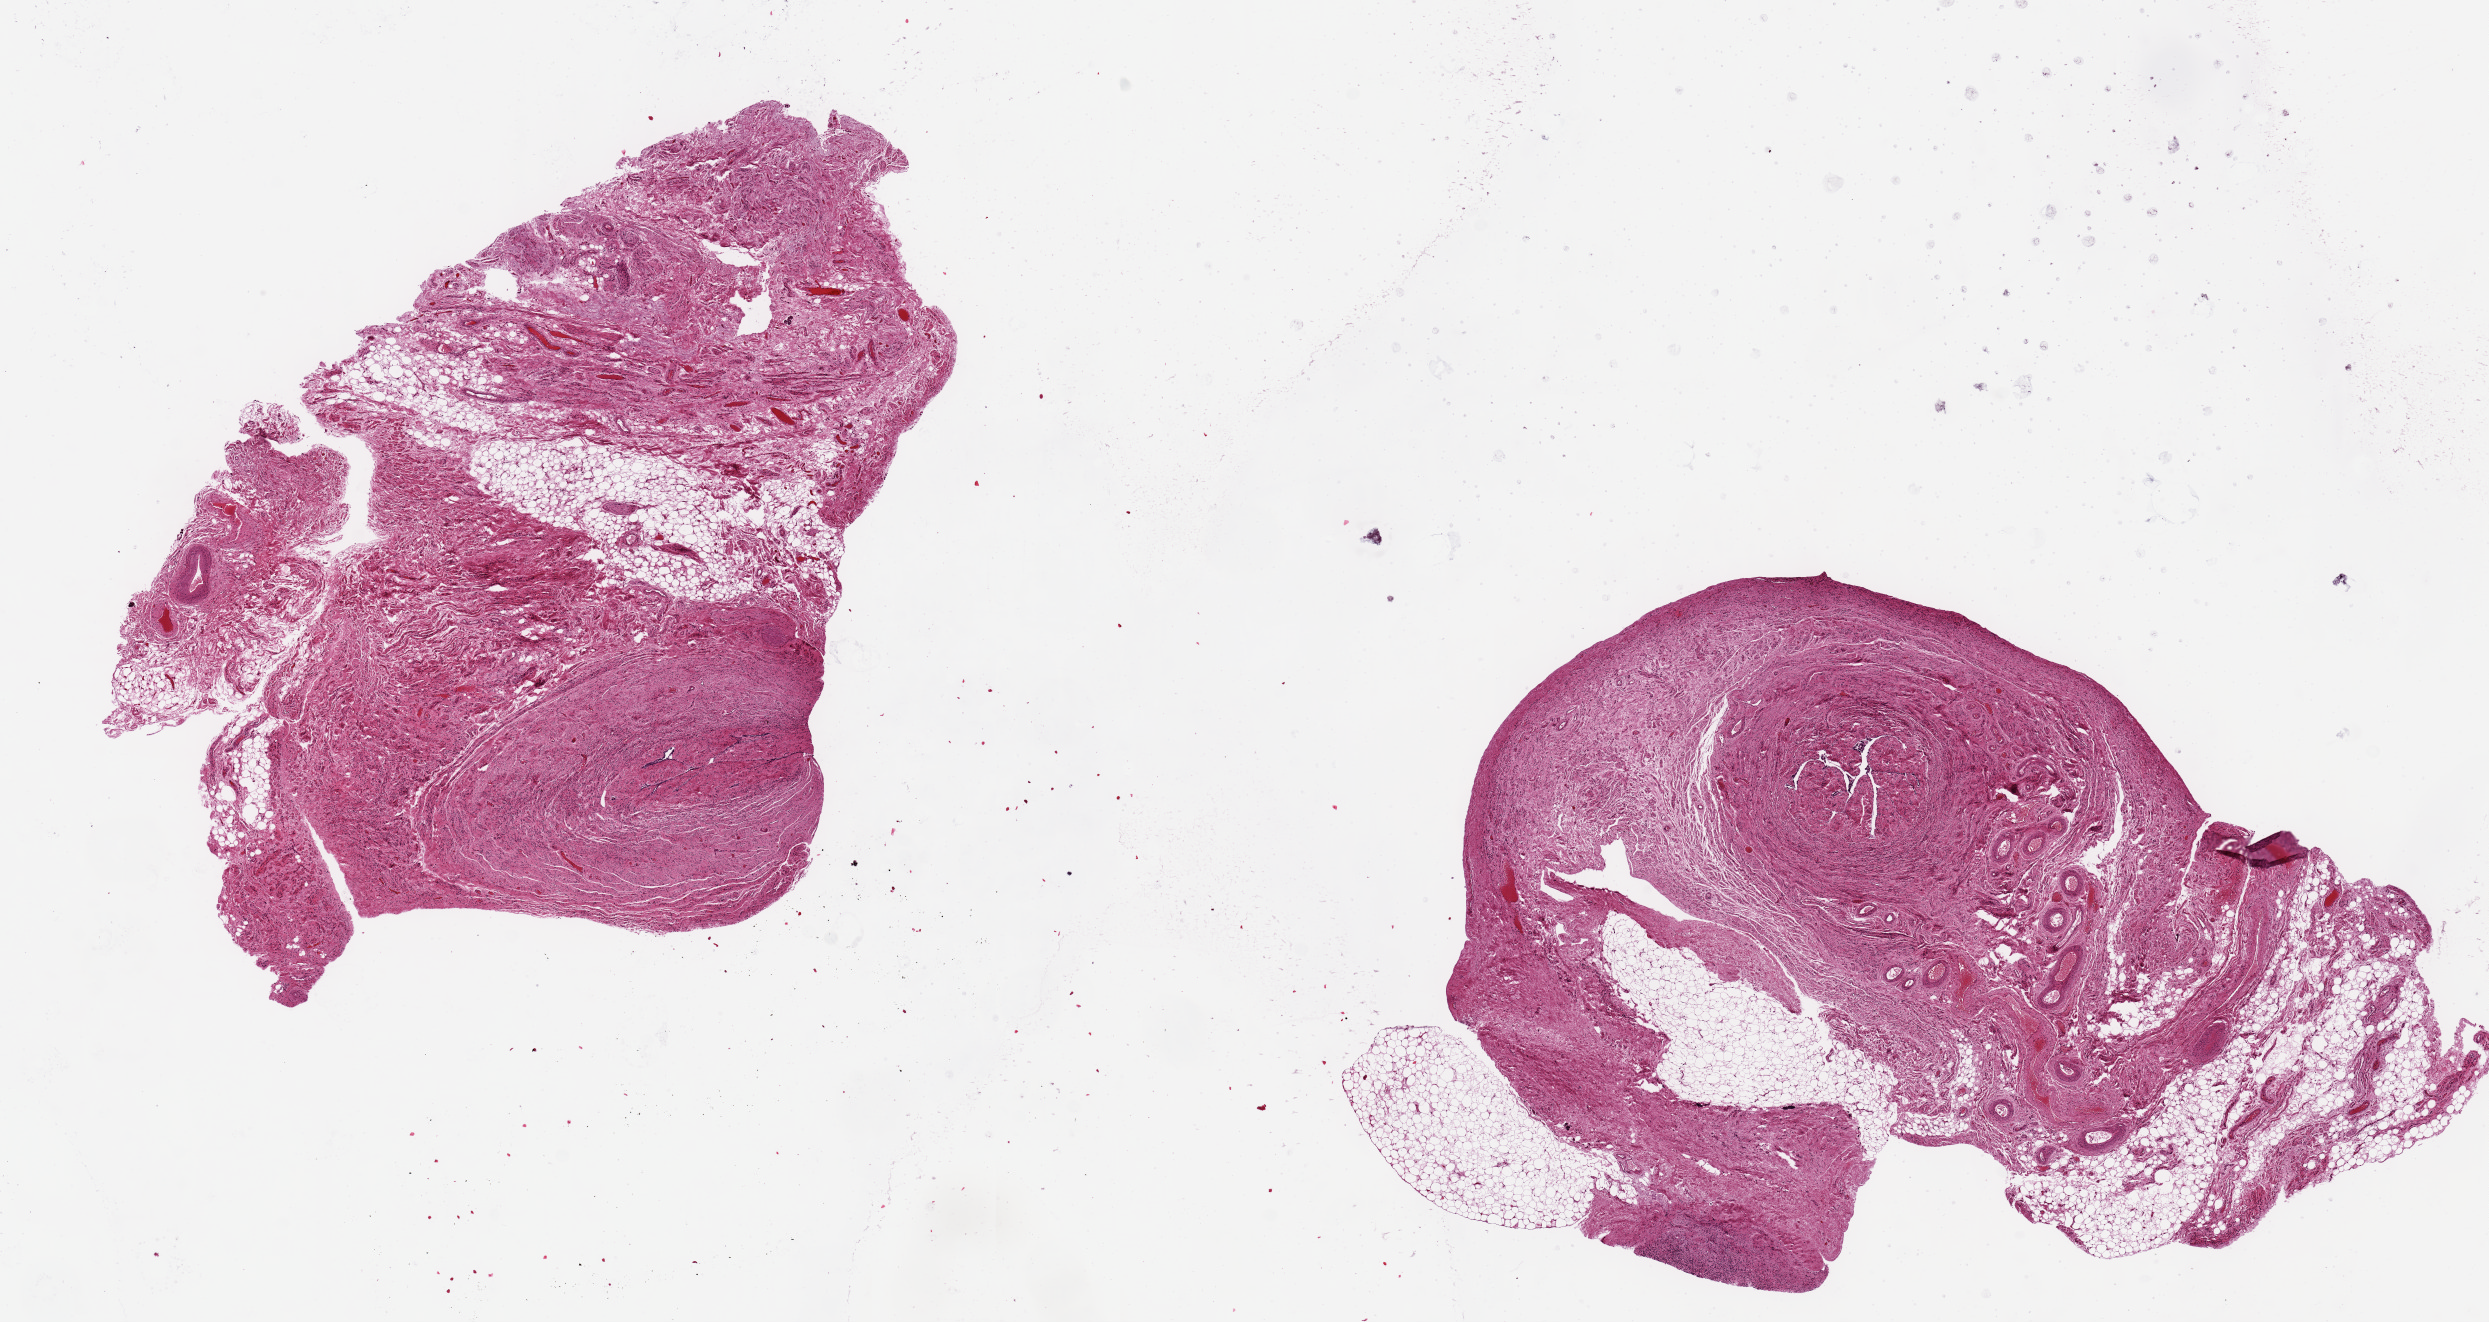
Digitized hematoxylin and eosin (H&E)-stained section — whole scanned area (about 19.7 x 10.5 mm, from a 20x scan) shown as a low-resolution overview, PAXgene-fixed, paraffin-embedded tissue, target tissue: fallopian tube, tissue donor sample.
- review note (as recorded): Epithelium 100% autolyzed (???score 3???)